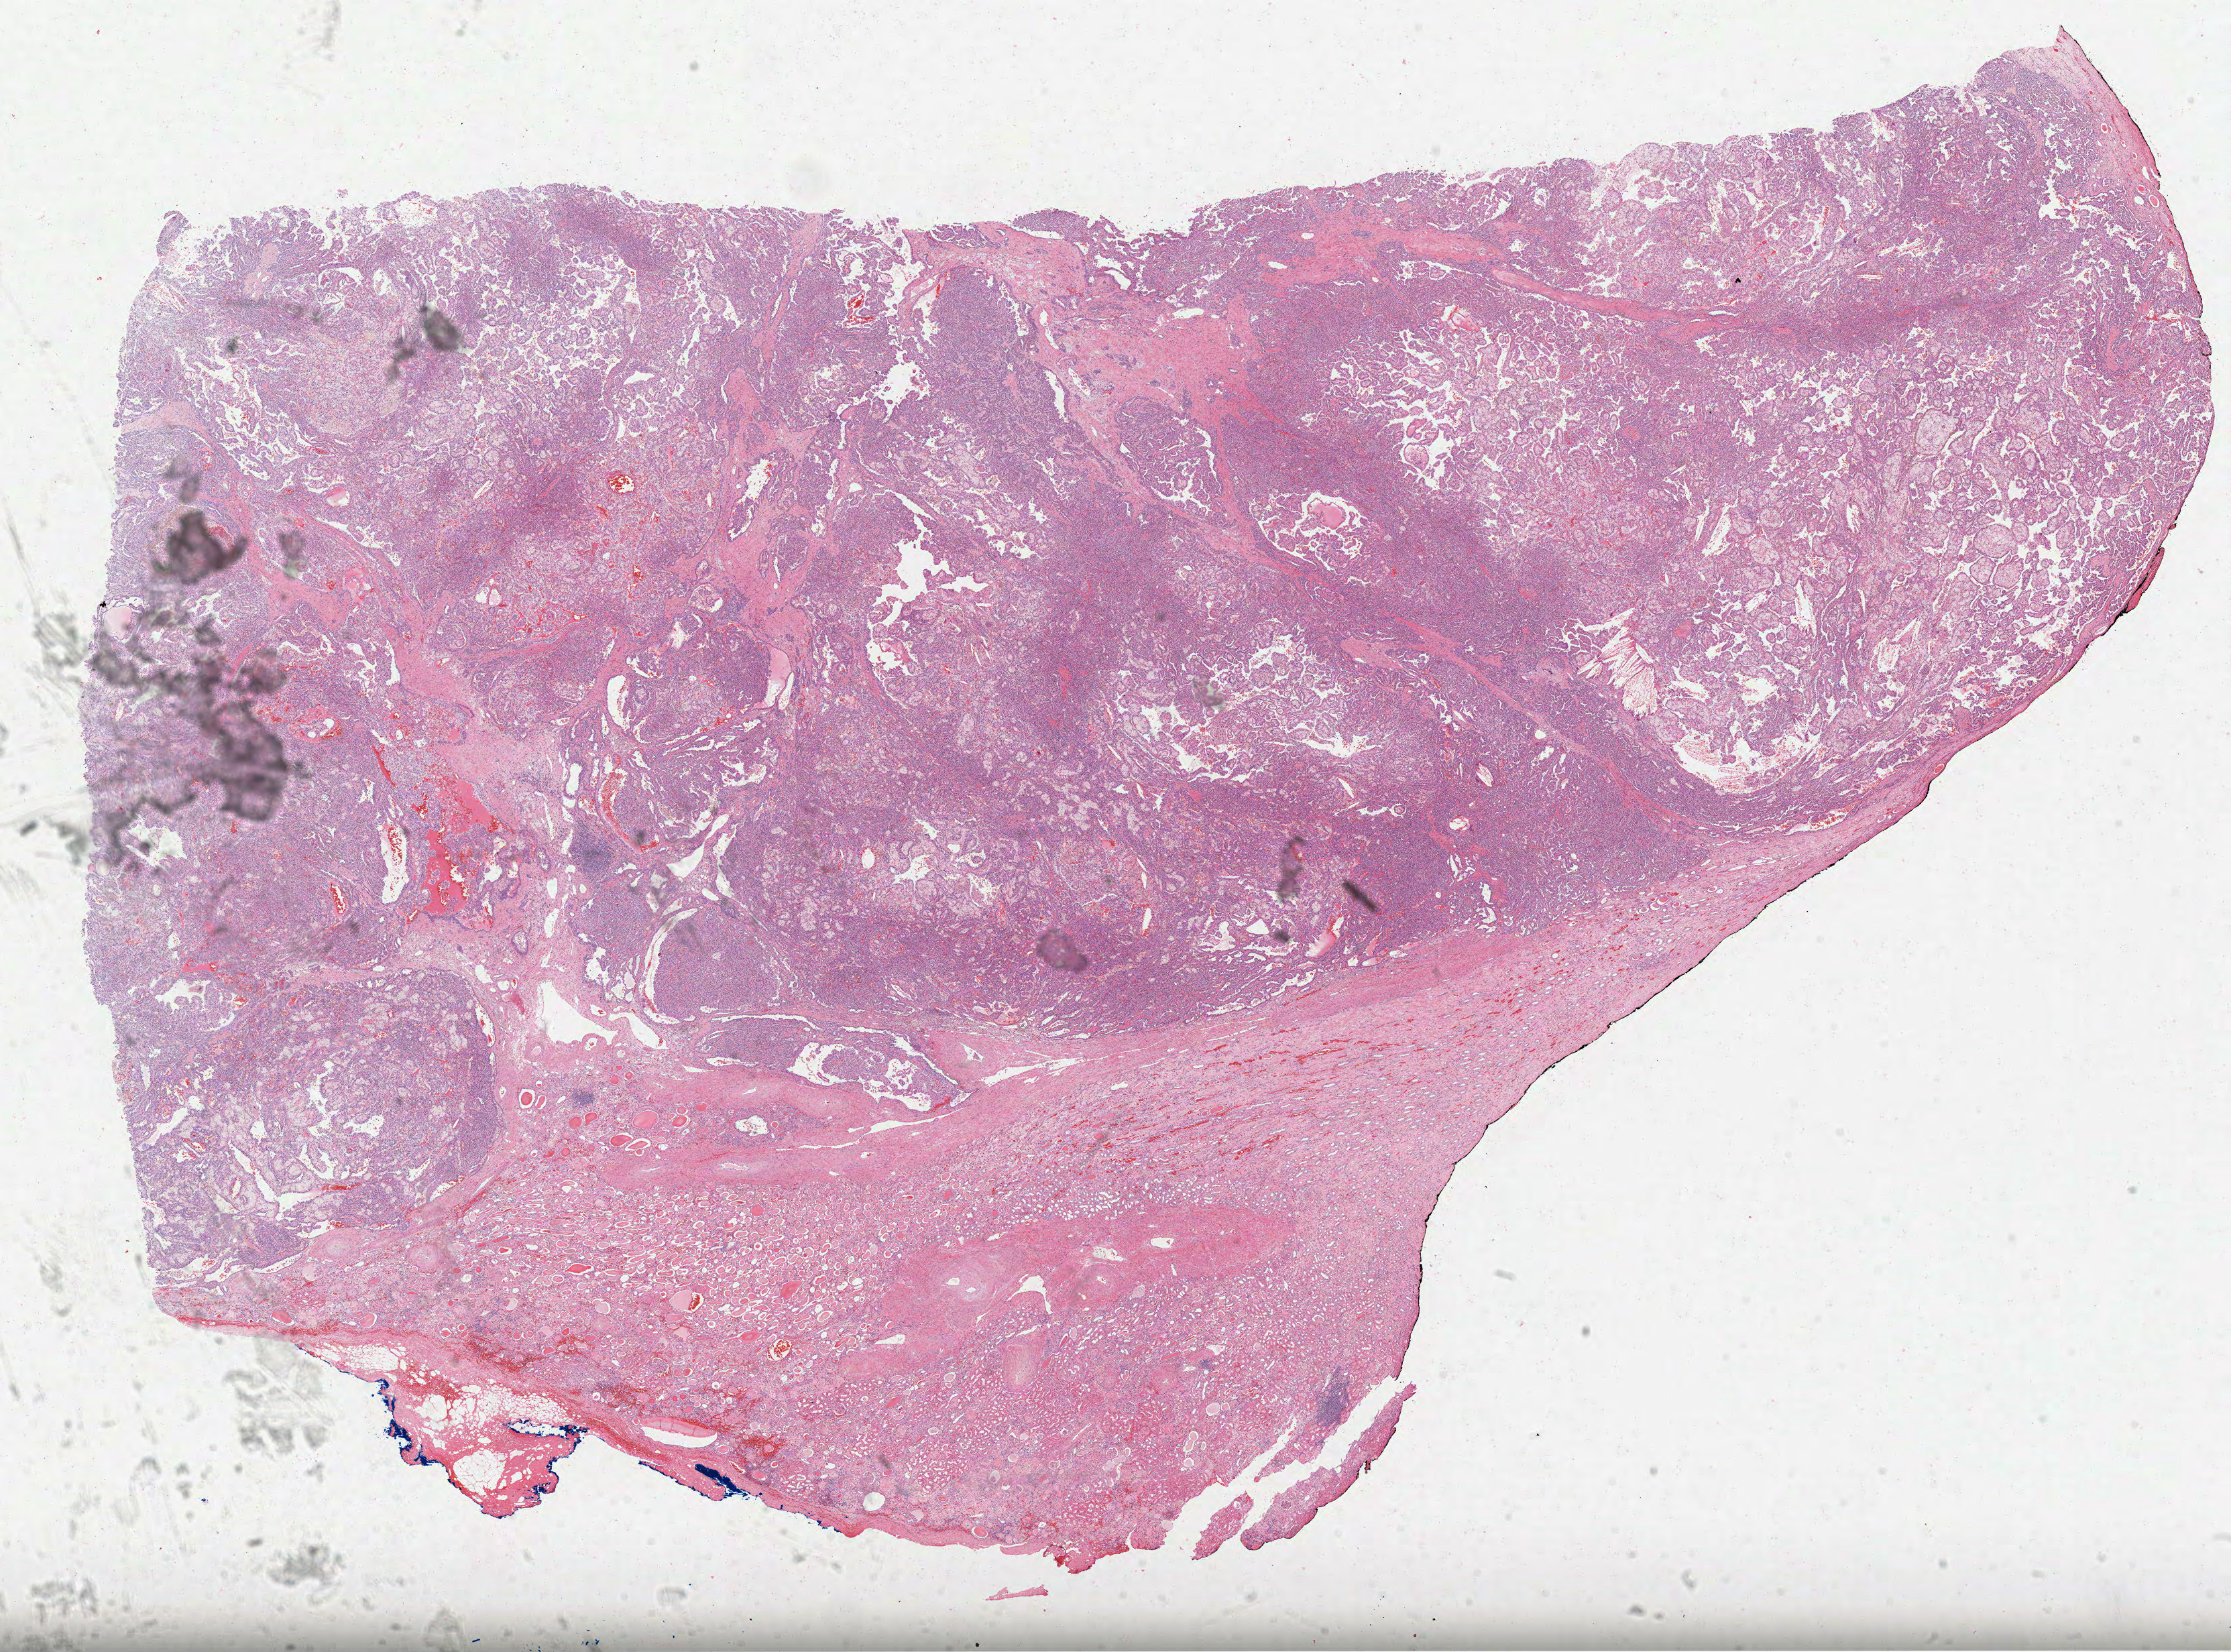
Digitized Hematoxylin and eosin (H&E) stained tissue section (whole slide) — whole scanned area (about 26.8 x 19.9 mm, slide scanned at 40x) shown as a low-resolution overview. FFPE section. Kidney, primary tumour sample. Male patient; age at initial diagnosis 83 years.
AJCC pathologic stage: I. Laterality: left. Histologic diagnosis: Papillary adenocarcinoma, NOS.